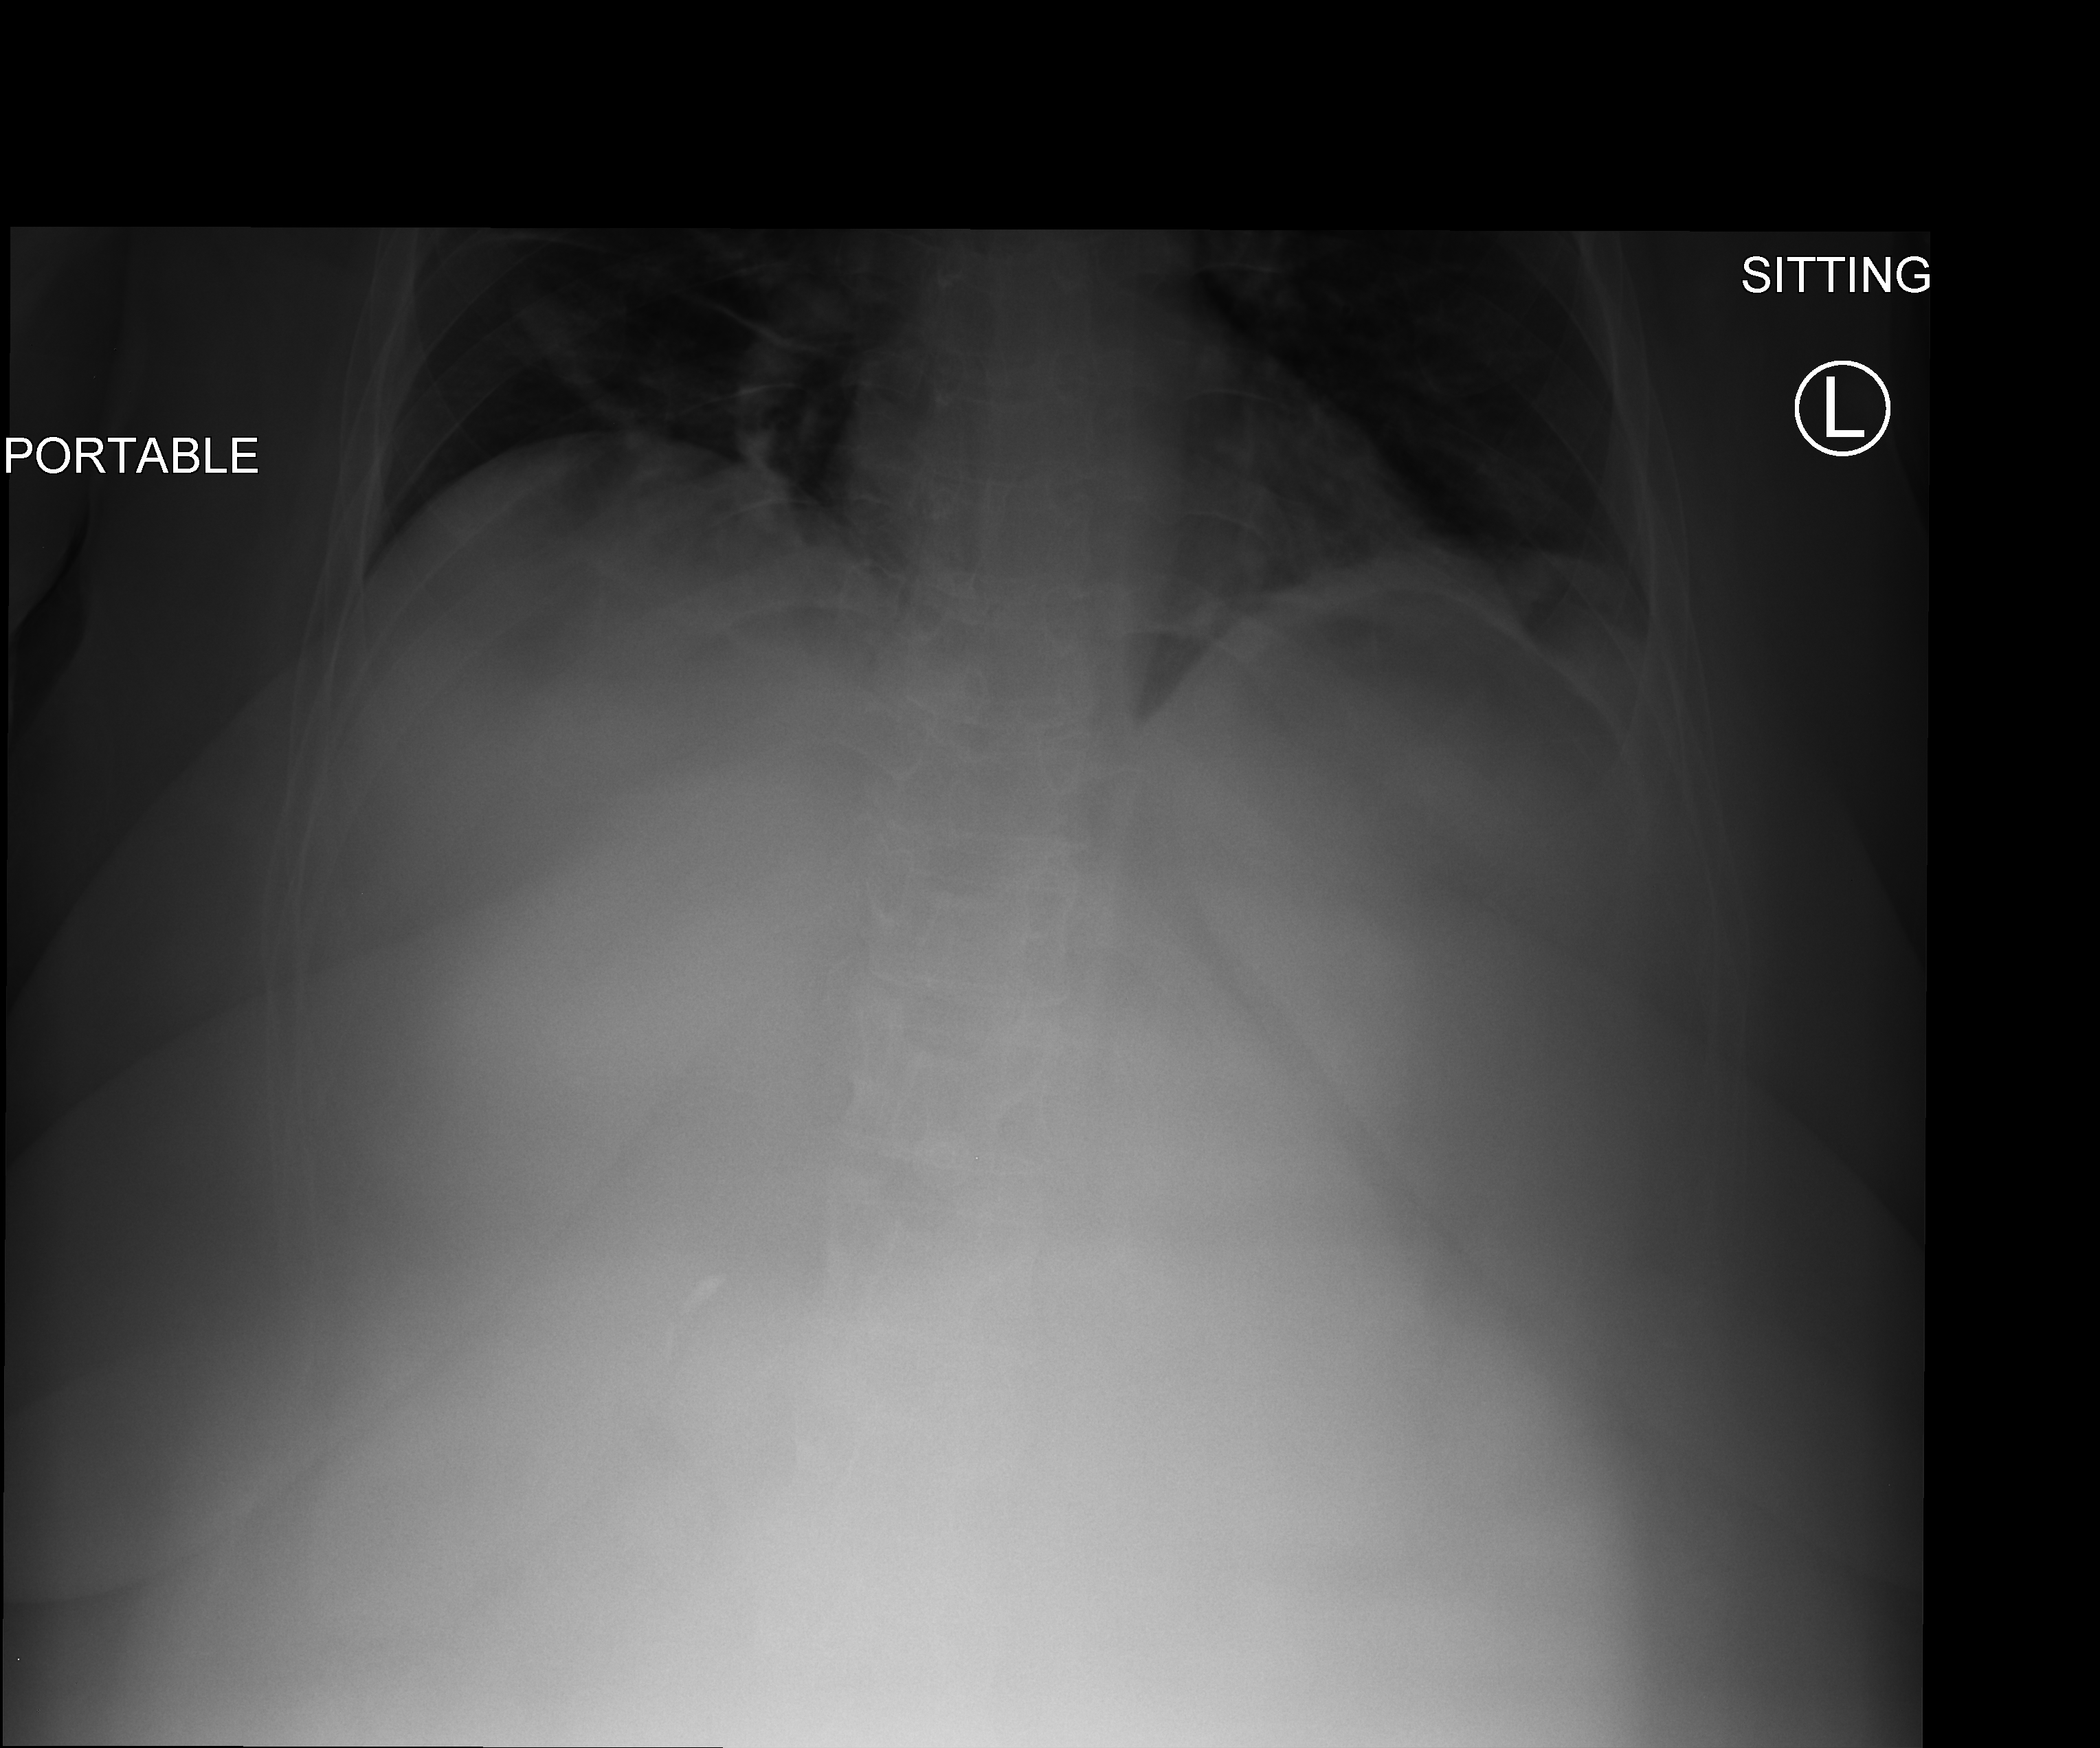
Abdomen X-ray (portable), anteroposterior (AP) projection. Patient hospitalised with COVID-19; female, aged 18–59 years.
Hospital-stay facts (about this admission, not read from this image; timing relative to this image not recorded): mechanically ventilated during this hospital stay: no.